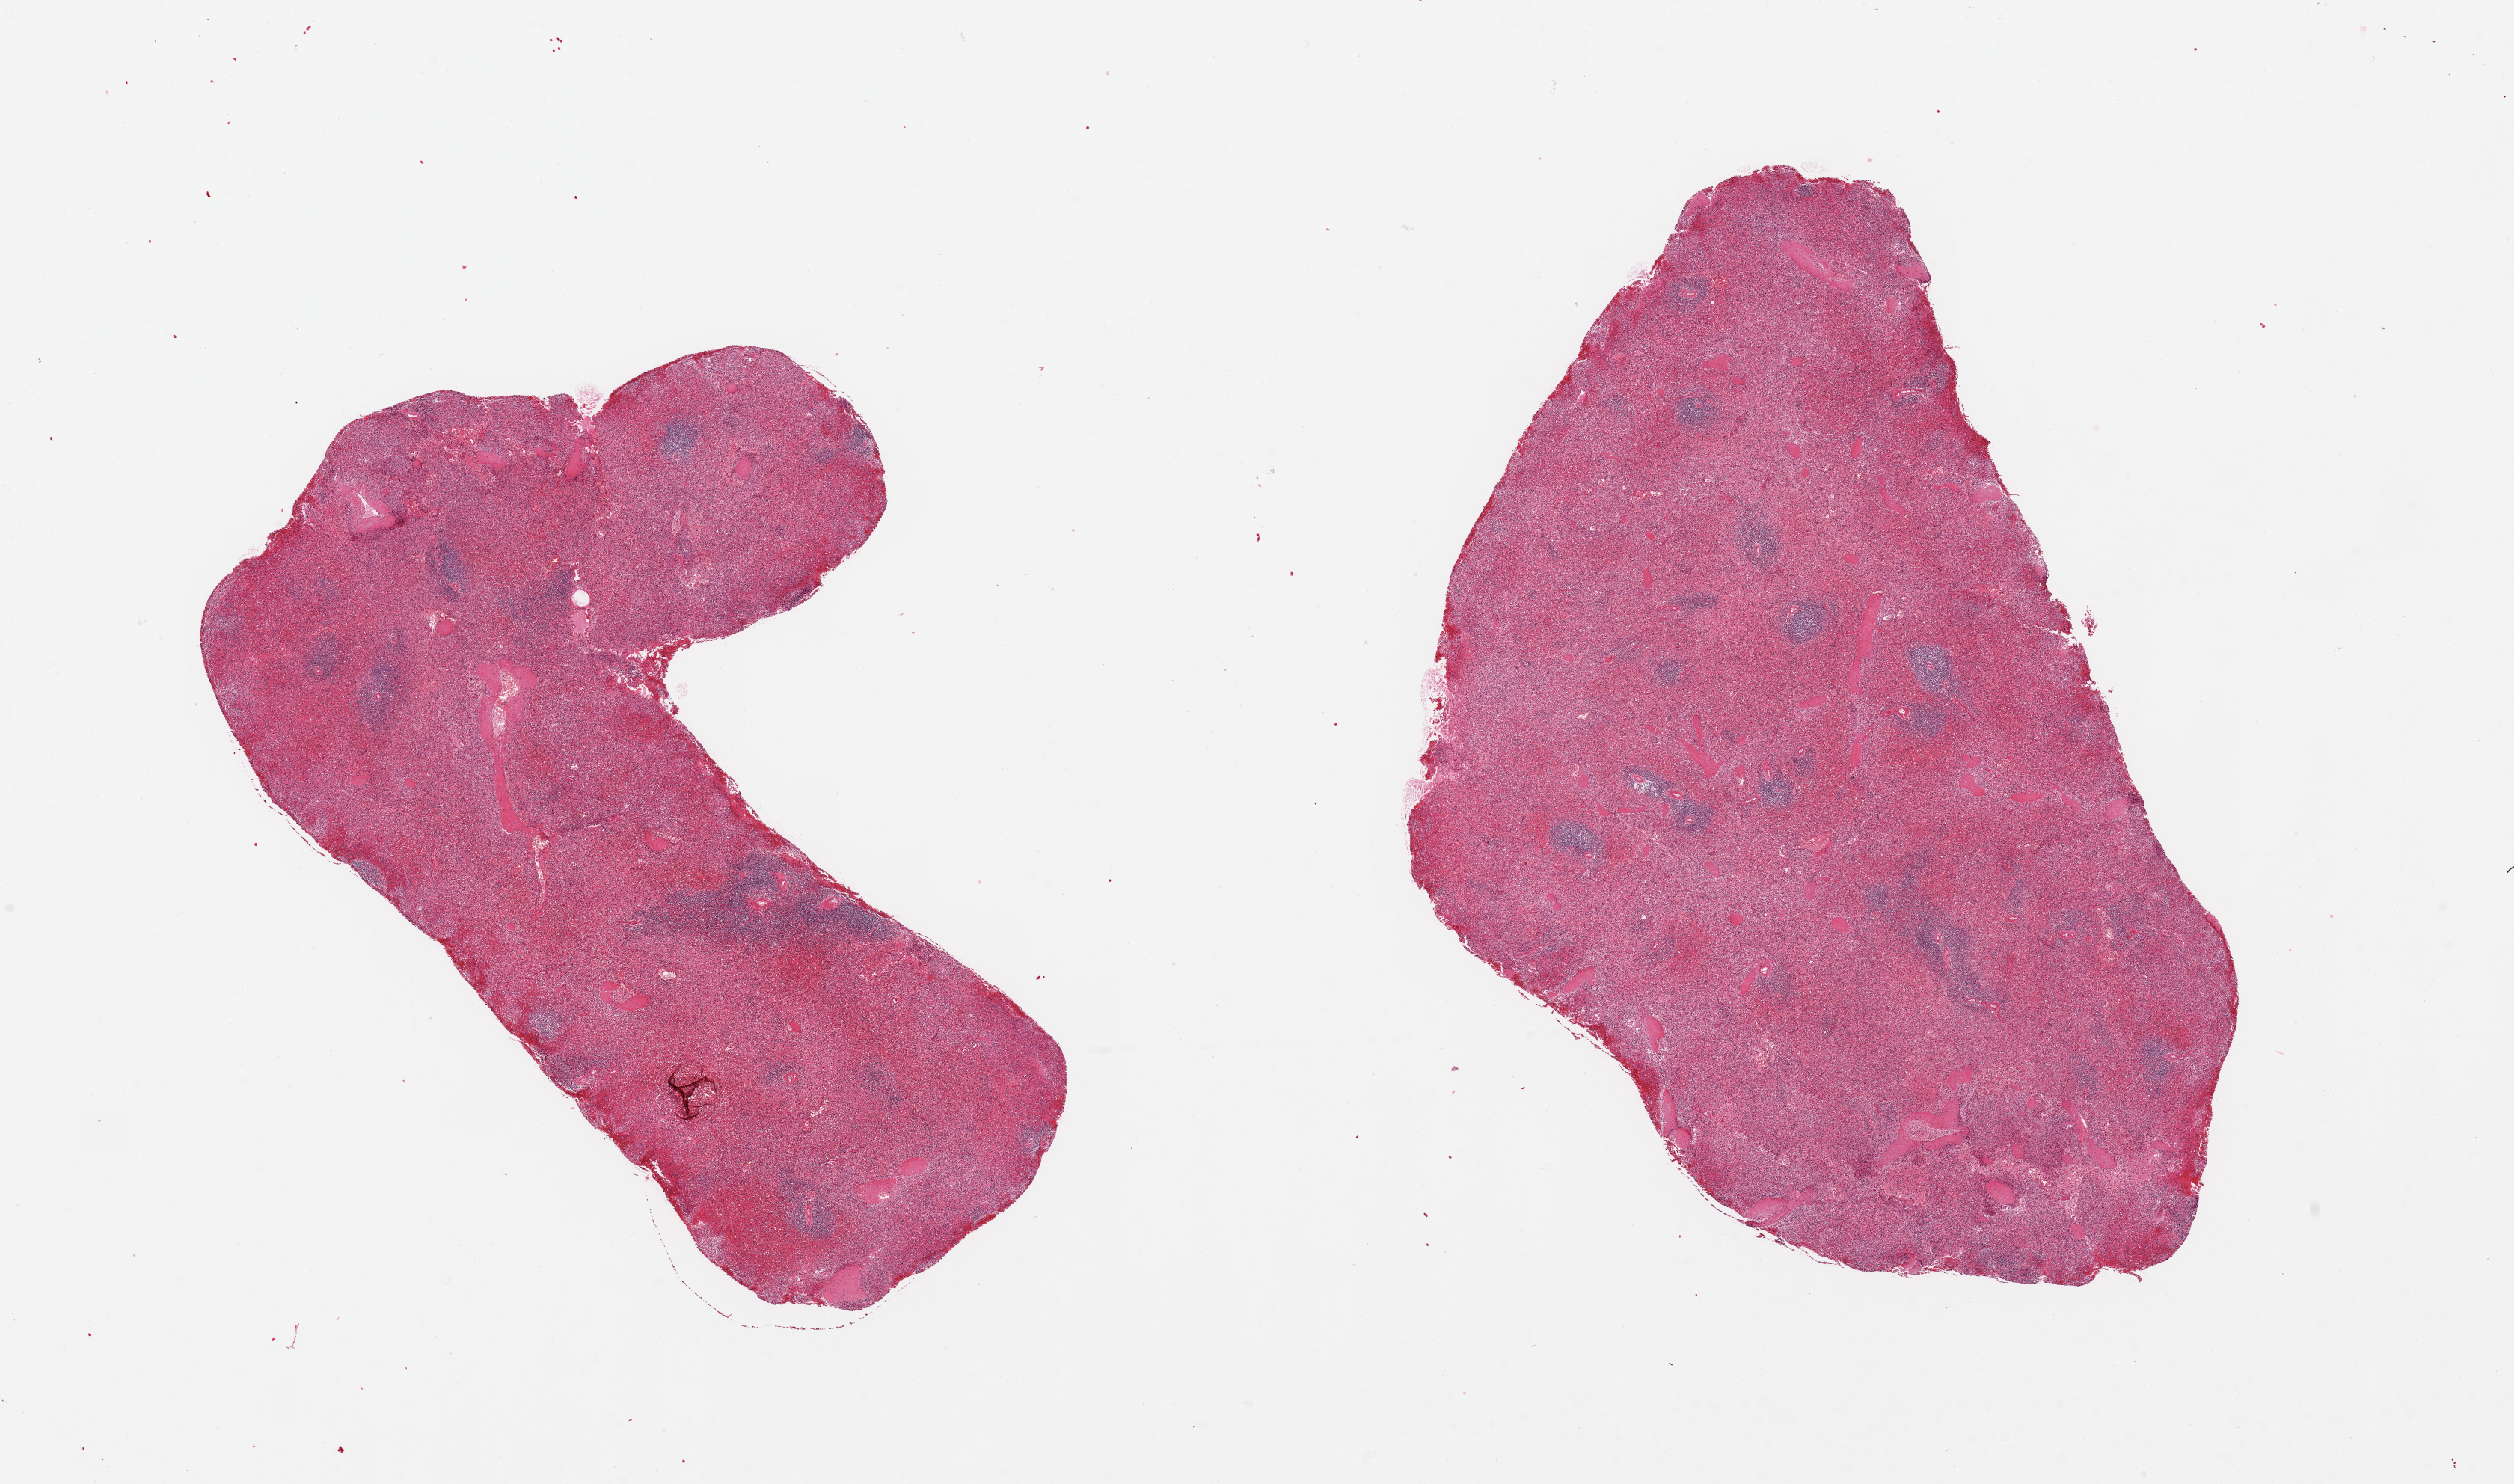
Whole-slide image, H&E stain, brightfield — shown as a low-resolution overview of the whole scanned area (about 26.6 x 15.7 mm), PAXgene-fixed, paraffin-embedded tissue, section of spleen (target tissue), donor tissue sample.
Pathologist's review note for this sample: 2 pieces, moderate congestion.